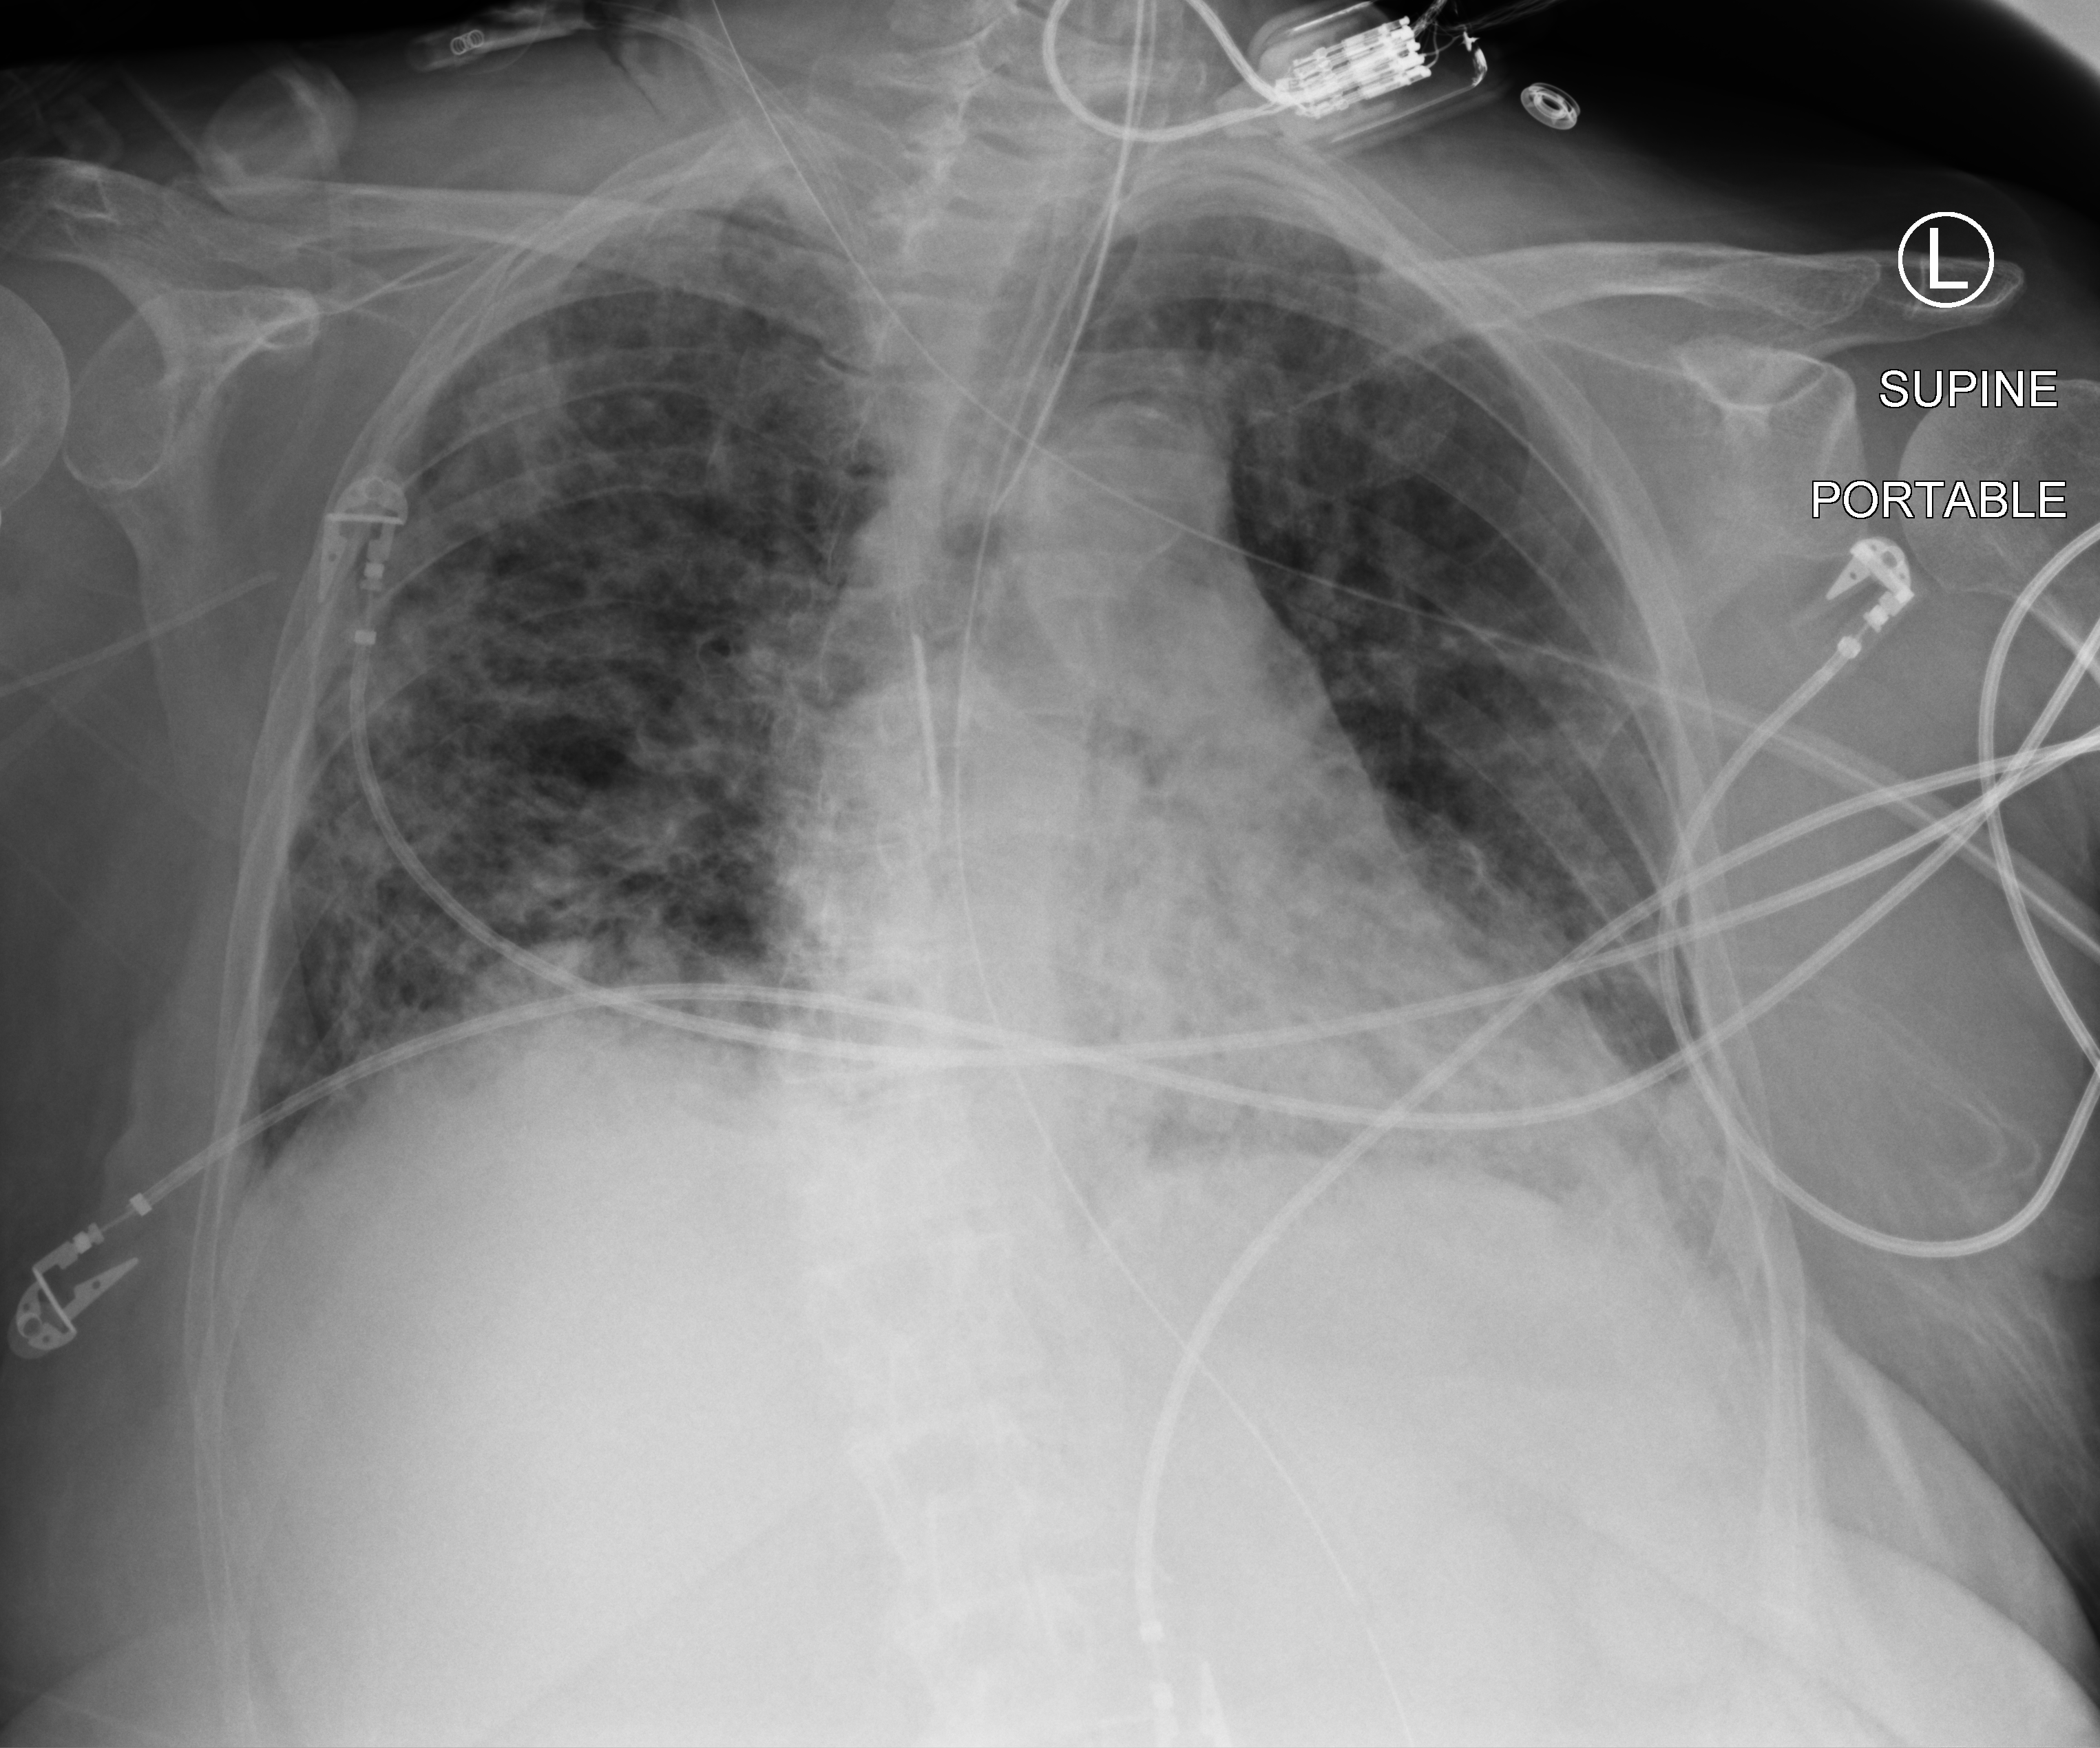
Bedside chest radiograph (computed radiography), anteroposterior (AP) projection. Patient hospitalised with COVID-19; female, aged 75–90 years.
From the hospital-stay record, not from the radiograph (when in the stay this image was taken is not recorded): length of hospital stay: 28 days.